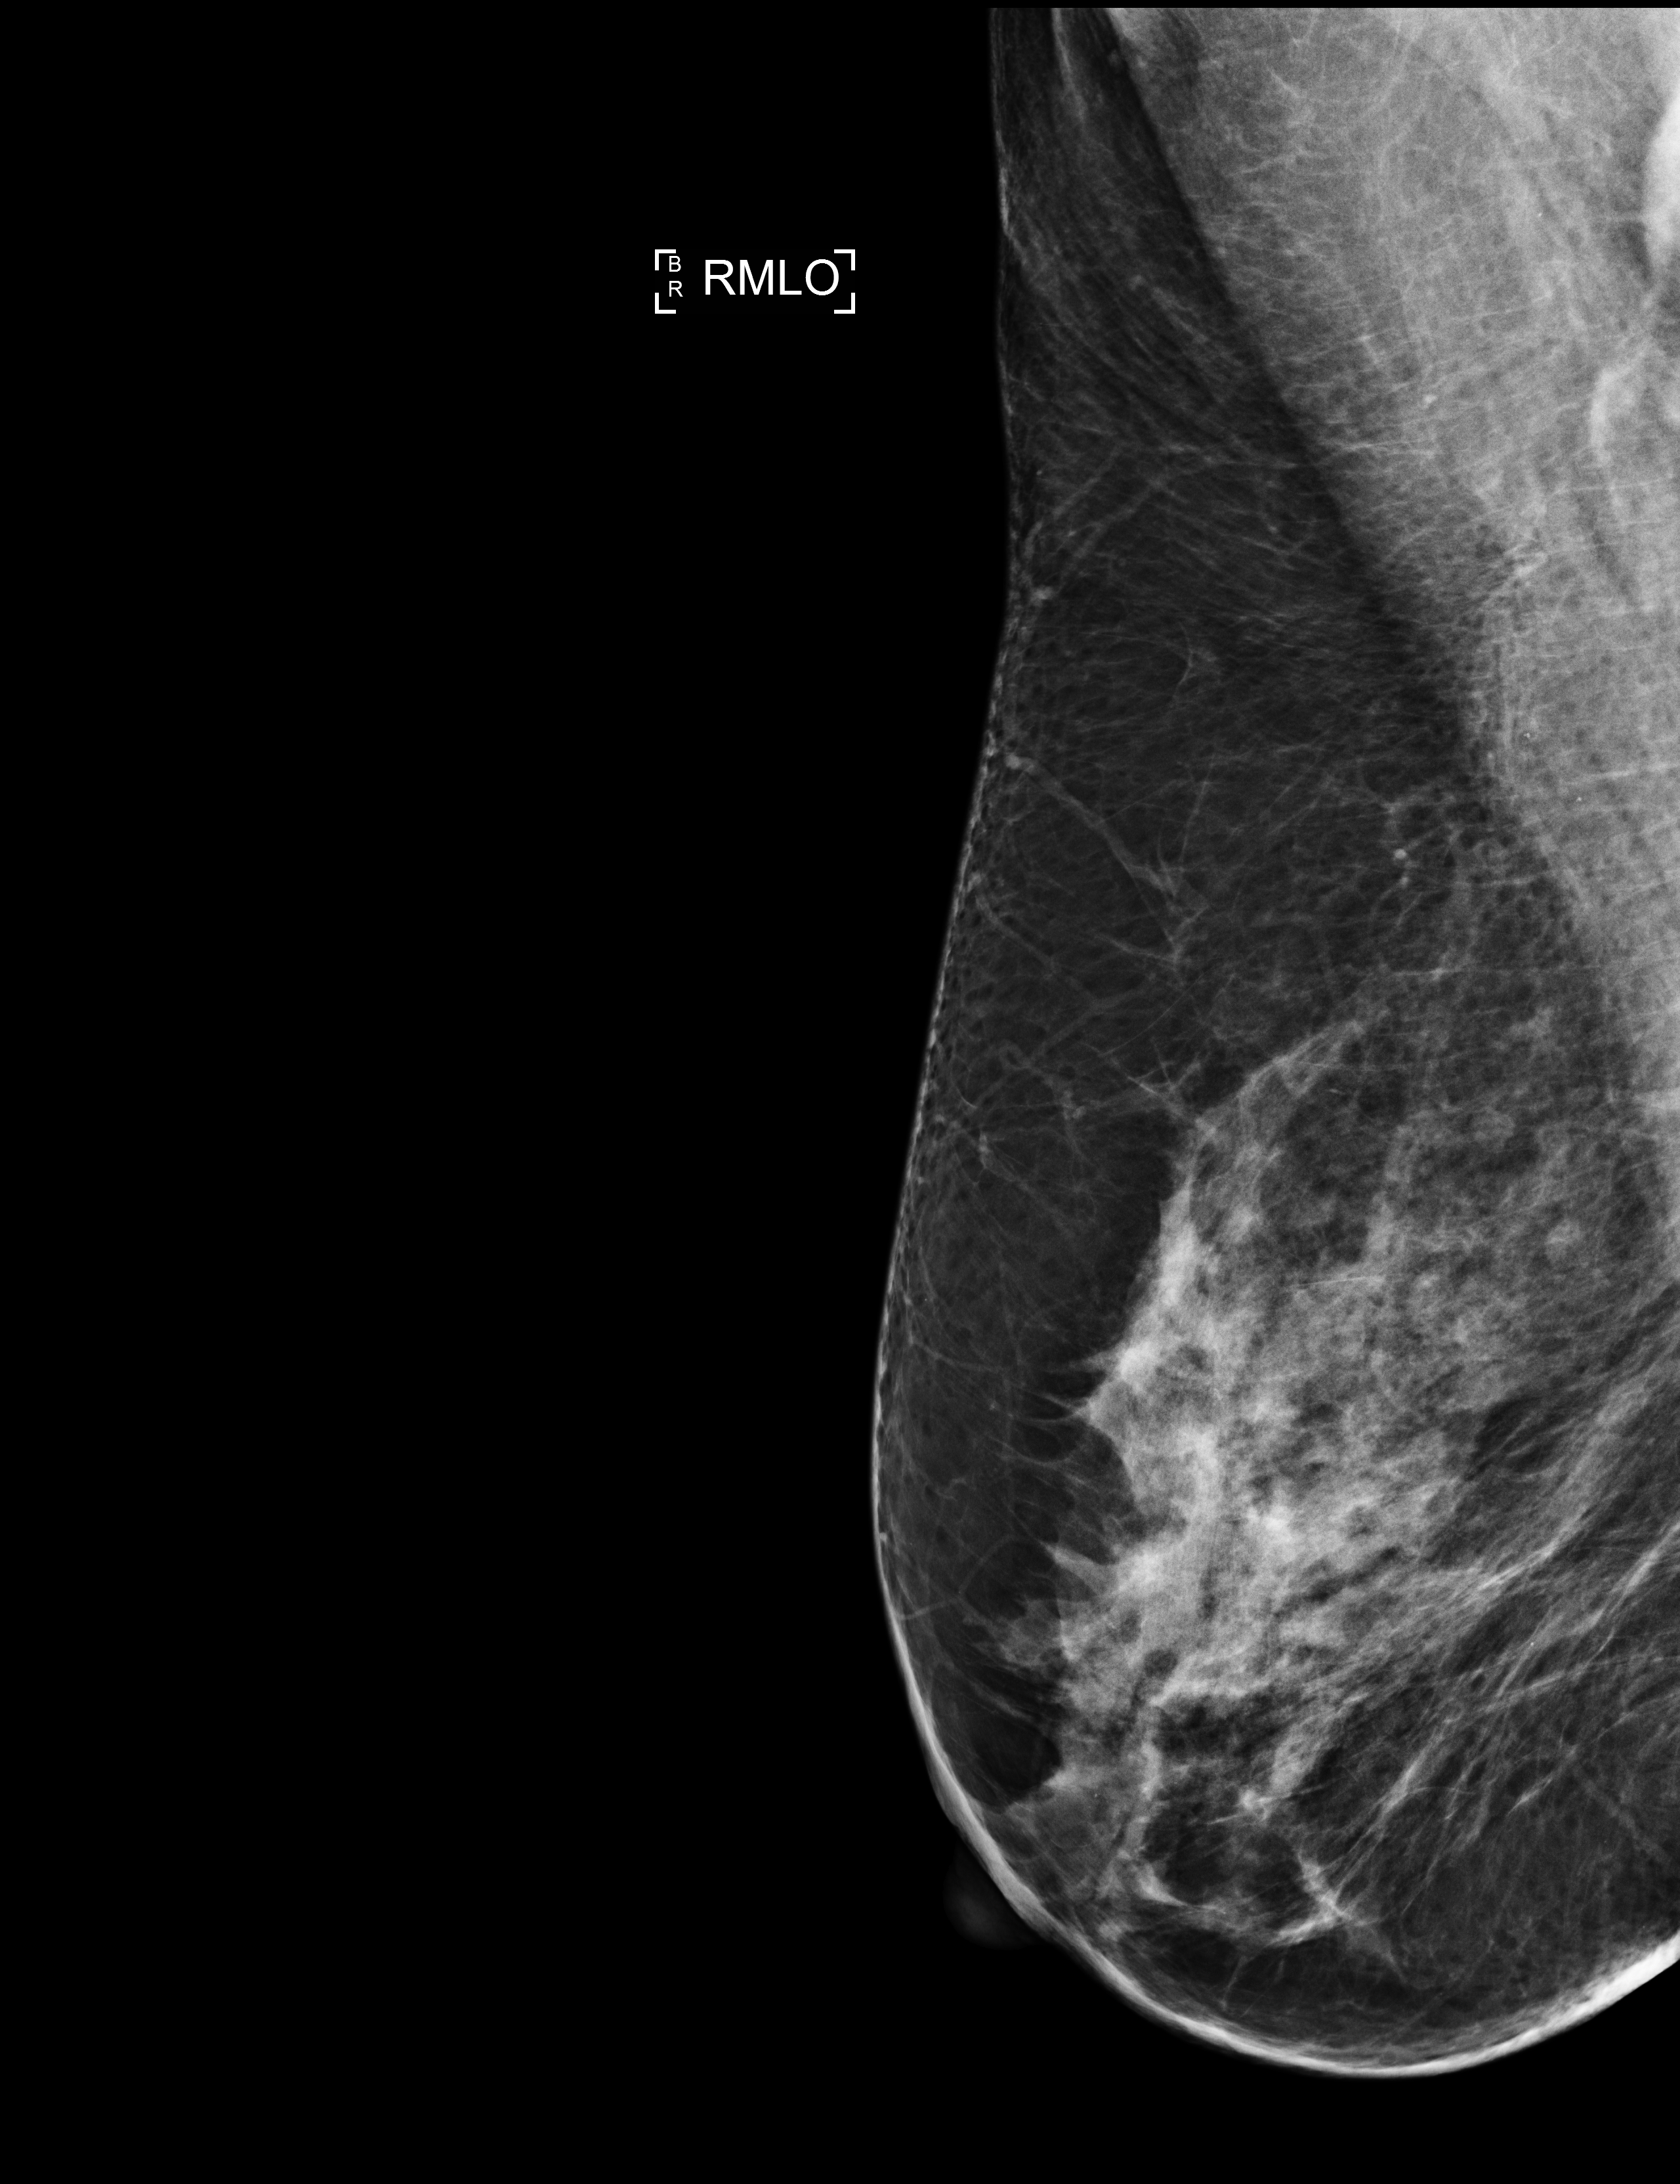
Annual screening mammography examination. Patient aged 56 years (female).
Image type: full-field digital mammogram. Breast: right. Projection: medio-lateral oblique projection.